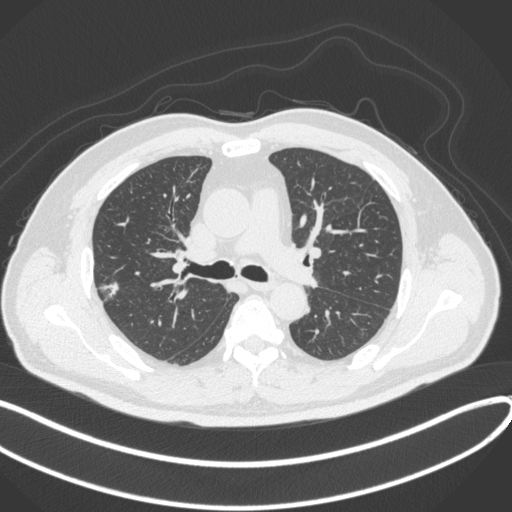
Chest CT, one axial slice; position 215 of 373 along the scan axis; 120 kVp; lung window (W 1500 / L -600 HU); 512 × 512 image matrix, field of view 400 × 400 mm. Male patient, age 60 years. Case-level facts recorded for this patient, not image findings: clinical TNM (as recorded): T1c N0 M0.
Annotated regions visible in this slice (bounding box drawn by a radiologist):
- lung tumour (recorded histology: adenocarcinoma): bounding box (x1, y1, x2, y2) in pixels: (93, 278, 124, 307)